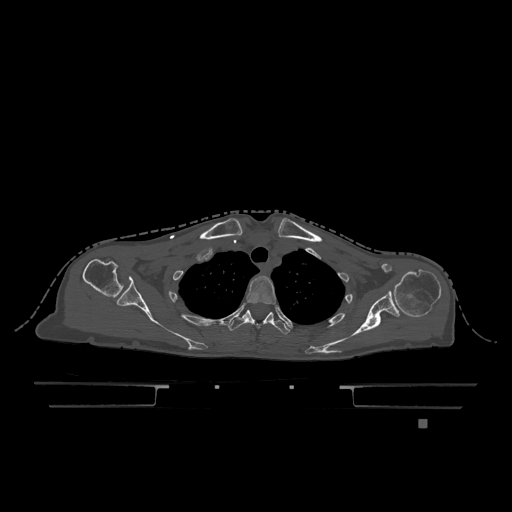
CT including the spine, one axial slice. Position 943 of 1317 along the scan axis. Bone window (W 1800 / L 400 HU). 0.5 mm slice thickness. 512 × 512 image matrix, field of view 500 × 500 mm. Patient: female, 74 years. Case-level facts recorded for this patient, not image findings: primary cancer: lung; vertebrae with lytic lesions (as recorded): T1, T4, T5, T6, L4, L5.
Structures marked on this image (semi-automatically segmented with operator editing):
- T2 vertebra: bounding box [x1, y1, x2, y2] px = [246, 276, 276, 305]
- T3 vertebra: [228, 310, 290, 335]
- T6 vertebra: [268, 312, 273, 315]